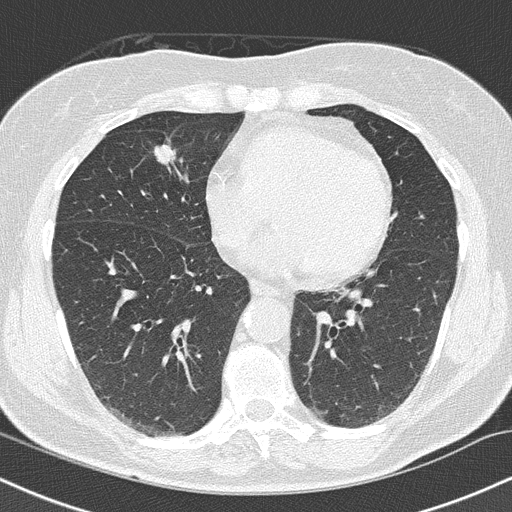
Axial slice from a low-dose chest CT screening exam, first (baseline) screen, lung window (W 1500 / L -600 HU), lung (sharp) reconstruction kernel (B50f), slice 86 of 145 in the series. Female, age 66 years at enrolment. Current smoker at enrolment.
- Lesion marked by an expert reader, bounding box (x1, y1, x2, y2) in pixels: (145, 132, 179, 166).
- Screening reader's record for this exam (one nodule recorded; not confirmed to be the boxed lesion): non-calcified nodule or mass ≥4 mm, right lower lobe, 10 × 8 mm, smooth margins, soft tissue attenuation.
- Official screen result: positive, change unspecified: nodule(s) >= 4 mm or enlarging nodule(s), mass(es), or other non-specific abnormalities suspicious for lung cancer.